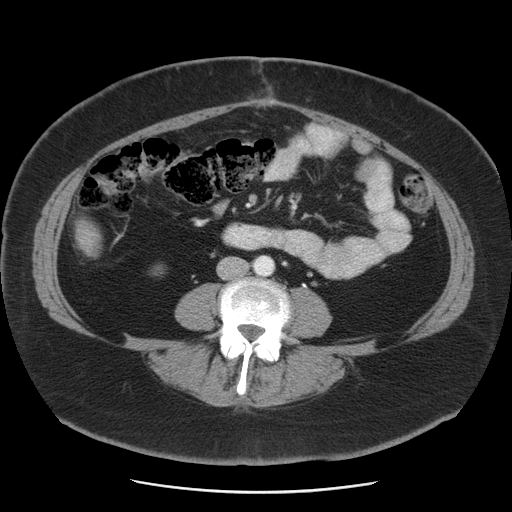
Contrast-enhanced abdominal CT, one axial slice. Position 4 of 55 along the scan axis. Soft-tissue window (W 400 / L 40 HU). 5 mm slice thickness. 512 × 512 image matrix, field of view 380 × 380 mm. Female patient, age 52 years. From the clinical record (not read from this slice): diagnosis: colorectal cancer liver metastases, imaged before liver resection; multiple liver metastases: yes; largest metastasis: 2.5 cm; disease in both lobes: yes.
Annotated regions visible in this slice (manually delineated by an expert):
- liver: bounding box (x1, y1, x2, y2) in pixels: (78, 220, 101, 255)
- planned liver remnant (the part of the liver to remain after resection): (76, 220, 102, 256)